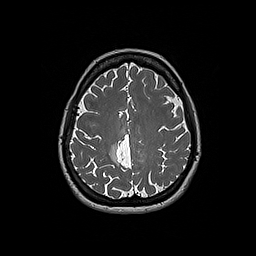
Brain MRI from a brain-tumour surgery series, one axial slice. Slice 62 of 192 in the series (ordered by position). 1 mm slice thickness. 256 × 256 image matrix. From the clinical record (not read from this slice): histopathology: Oligodendroglioma; WHO grade: 2; IDH mutation: yes; tumour location: Right Parietal.
Structures marked on this image (outlined manually by an expert reader):
- tumour: bounding box (x1, y1, x2, y2) in pixels: (110, 144, 119, 165)